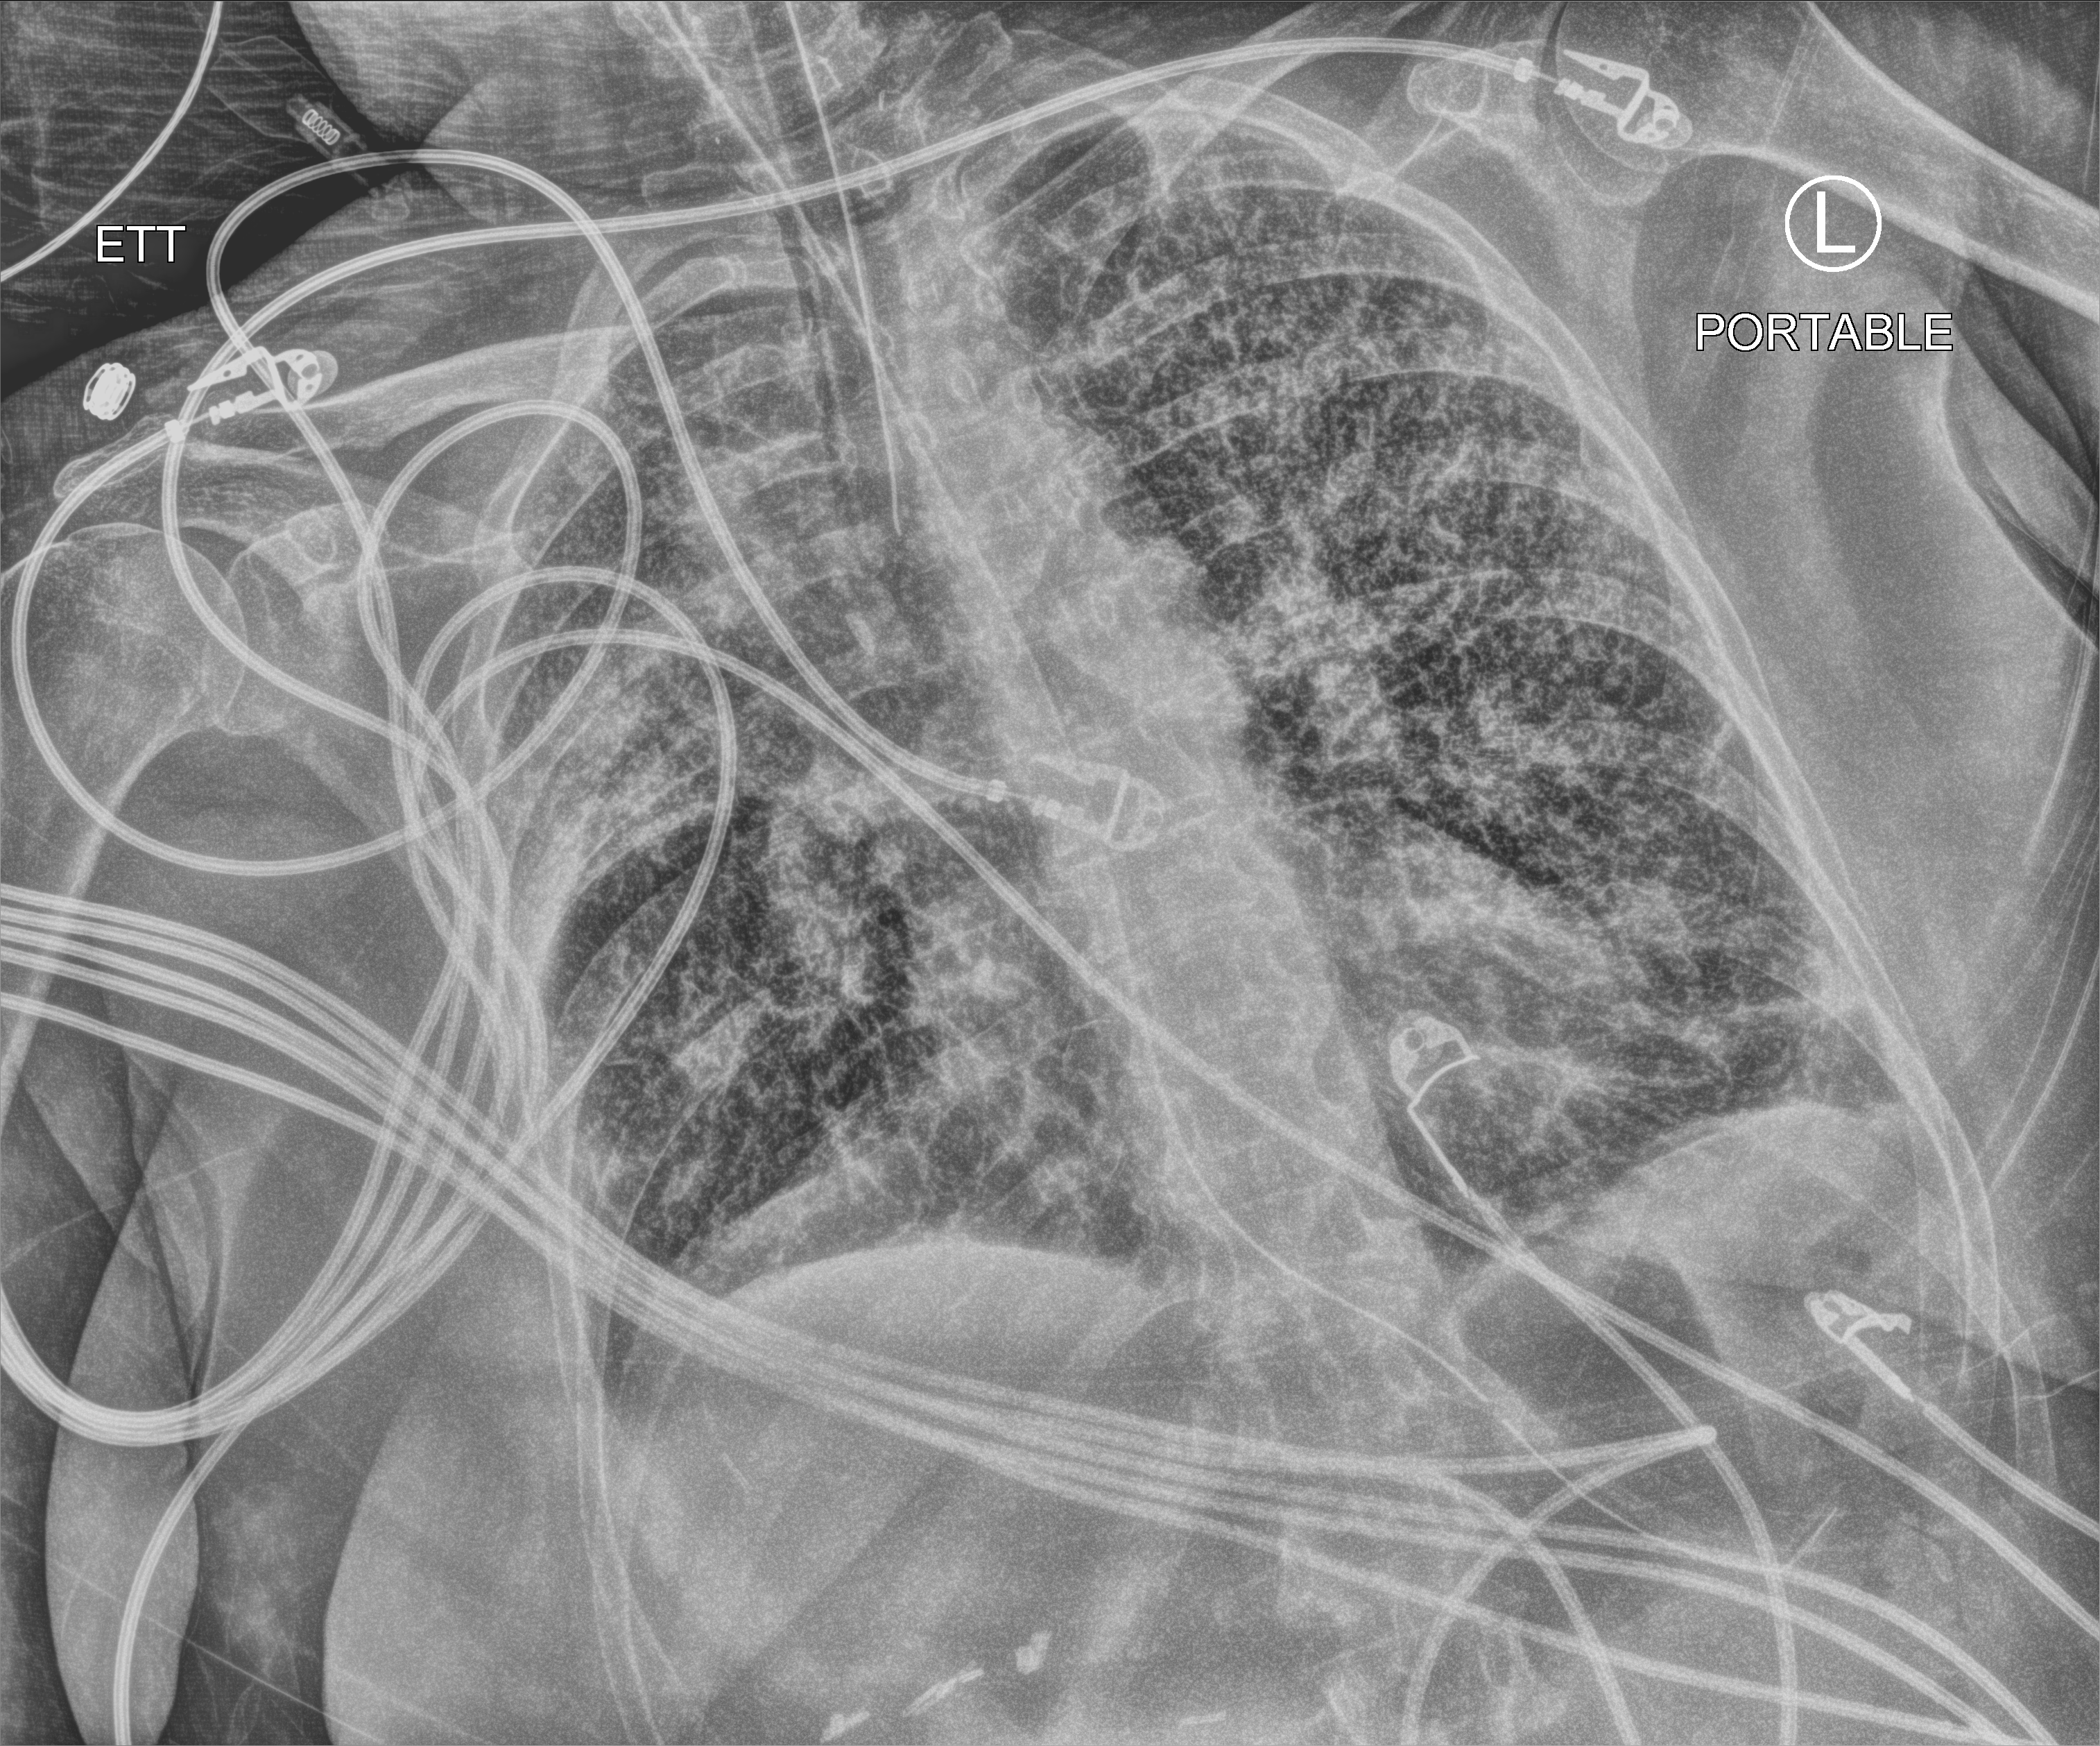
Bedside chest radiograph (computed radiography); anteroposterior (AP) projection. Female patient hospitalised with COVID-19, age 60–74 years.
From the hospital-stay record, not from the radiograph (when in the stay this image was taken is not recorded):
- admitted to intensive care during this hospital stay: yes
- length of hospital stay: 19 days